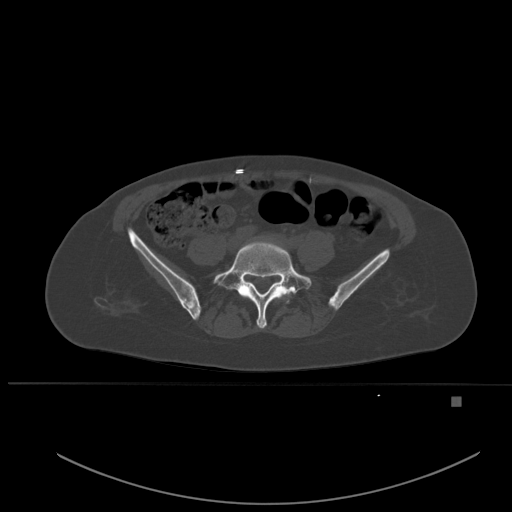
CT including the spine, one axial slice. Position 156 of 651 along the scan axis. Bone window (W 1800 / L 400 HU). 512 × 512 image matrix. Patient: female, 49 years. Case-level facts recorded for this patient, not image findings: primary cancer: breast; vertebrae with lytic lesions (as recorded): L3, T12, L4.
Outlined on this slice (semi-automatic segmentation, software-assisted and operator-edited):
- L5 vertebra: bounding box <213,241,312,329> (left, top, right, bottom; pixels)